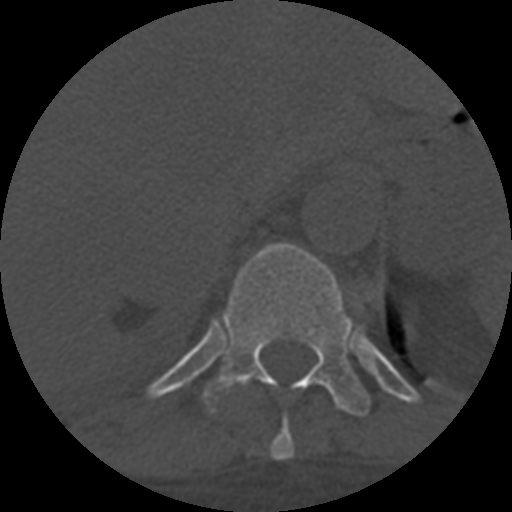
CT including the spine, one axial slice; position 342 of 708 along the scan axis; 120 kVp; one of 3 acquisitions stored at this slice position; bone window (W 1800 / L 400 HU); 512 × 512 image matrix, field of view 160 × 160 mm. Patient age 55 years. From the clinical record (not read from this slice): primary cancer: colon; vertebrae with lytic lesions (as recorded): T12, L1, L5.
Outlined on this slice (semi-automatic segmentation, software-assisted and operator-edited):
- T10 vertebra: box from (x=270, y=417) to (x=295, y=461) px
- T11 vertebra: (x=203, y=243)–(x=371, y=417)